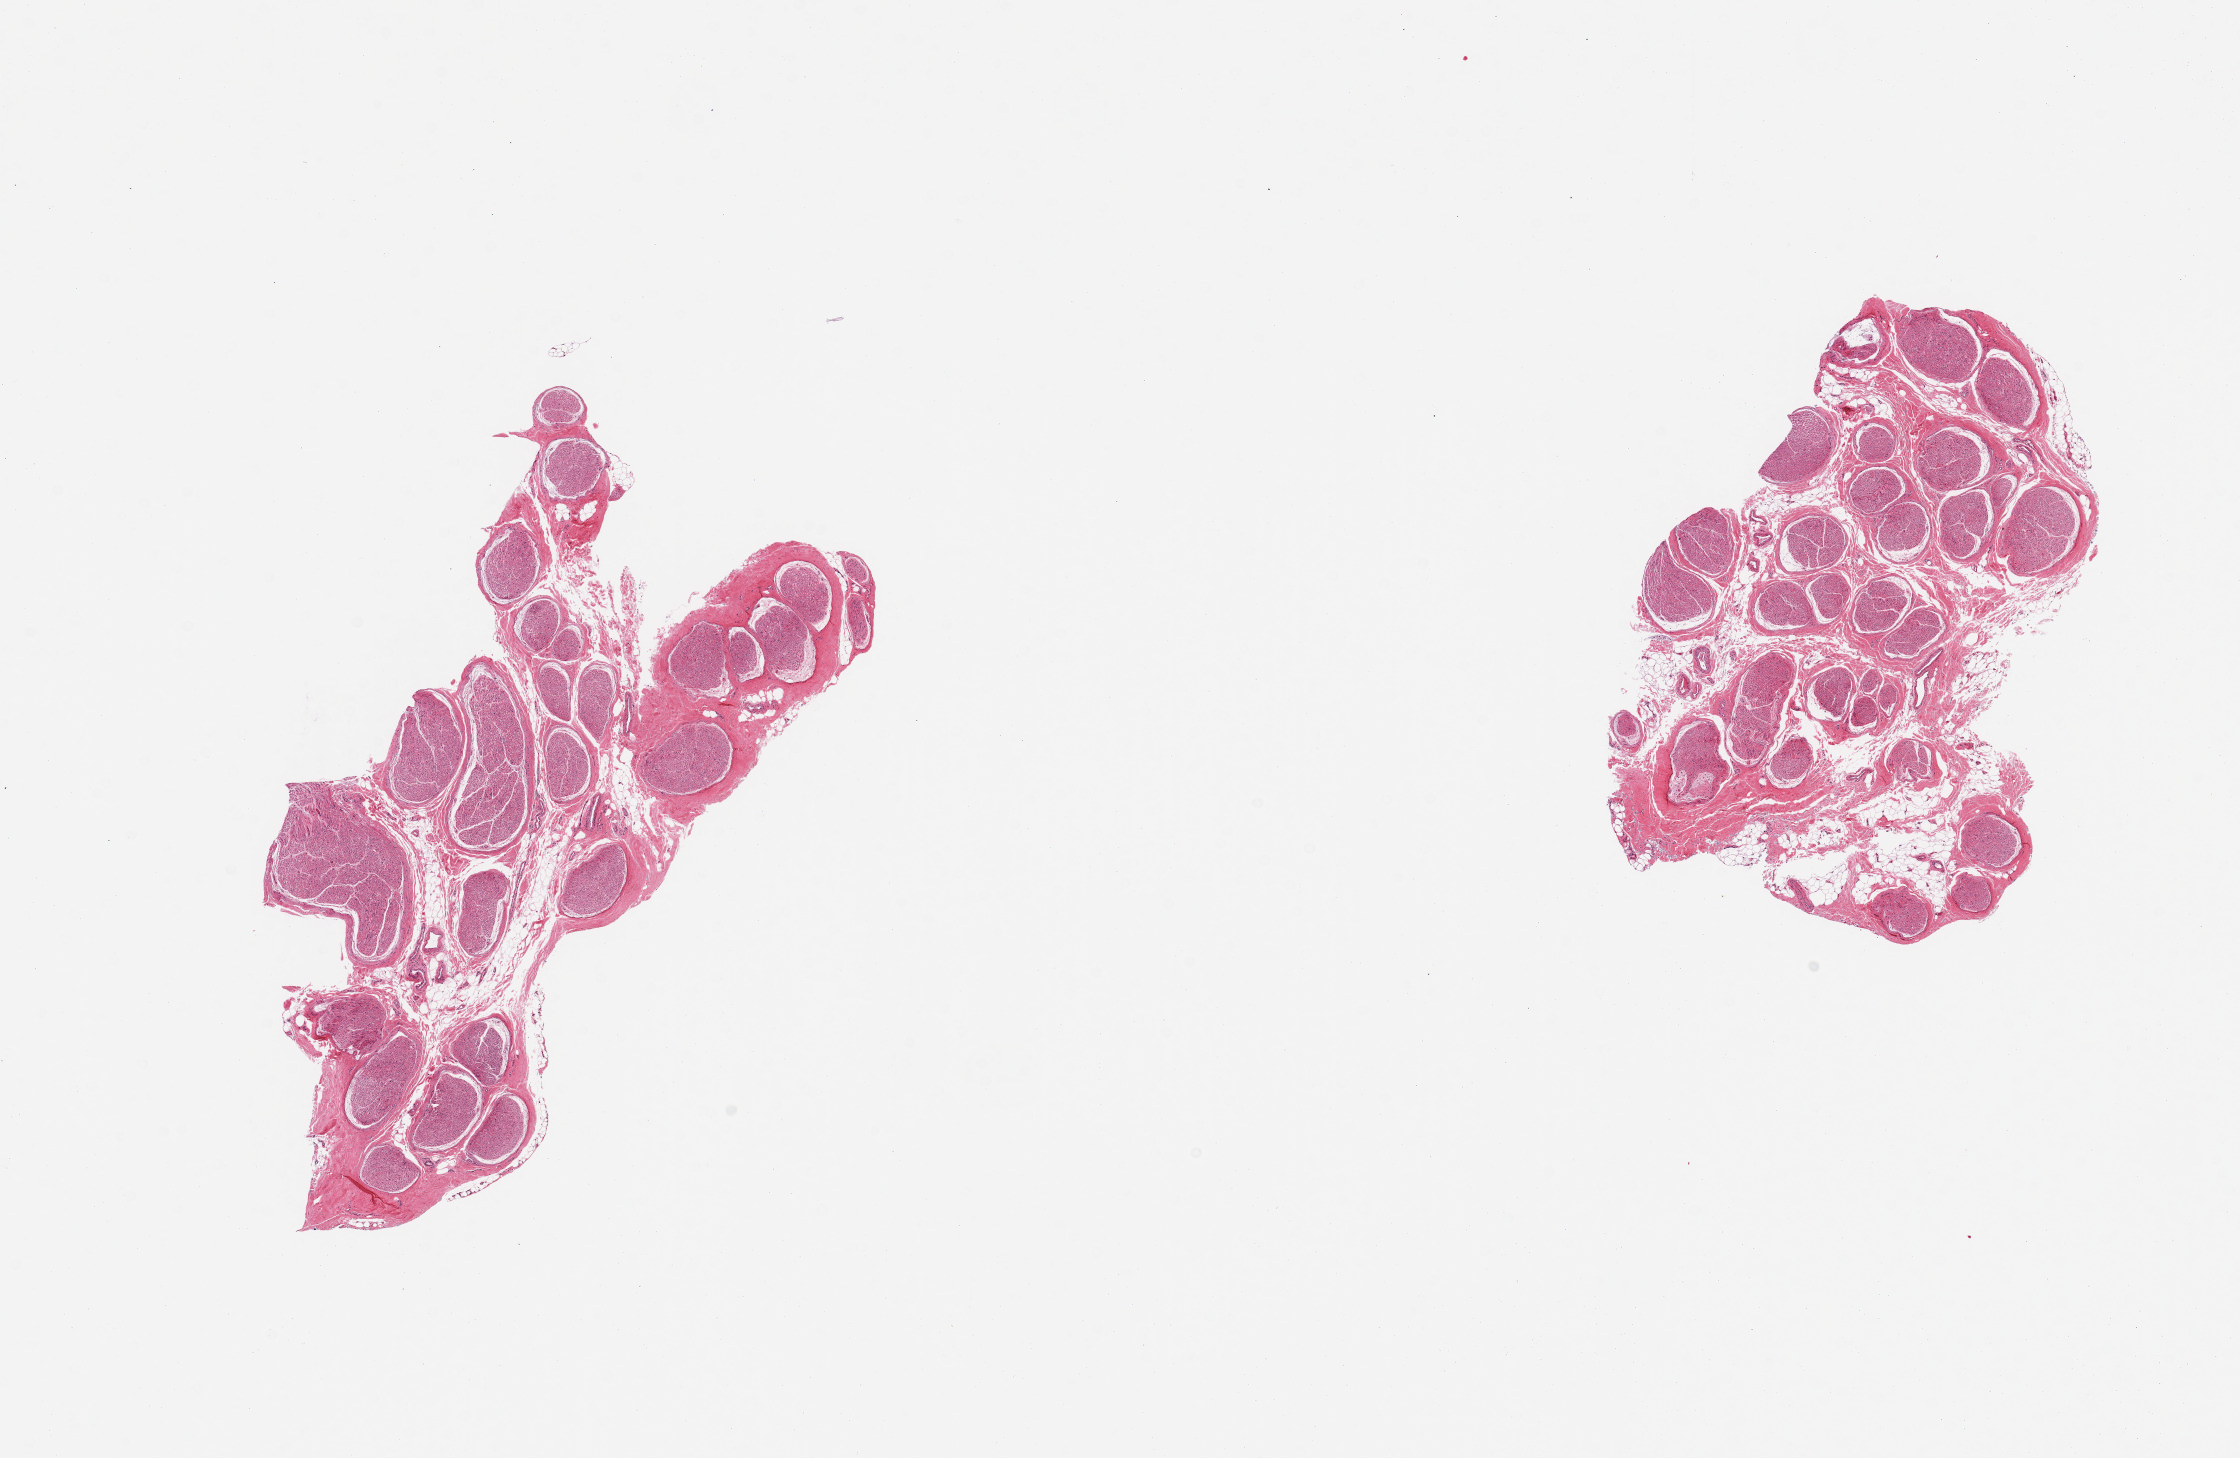
Whole-slide image, hematoxylin and eosin (H&E) stain, shown as a low-resolution overview of the whole scanned area (about 17.7 x 11.5 mm). PAXgene-fixed paraffin-embedded (PFPE) section. Sampled site (target tissue): tibial nerve. Donor tissue sample. Donor: male.
* pathologist's review note for this sample: 2 pieces; 10% & 20% internal fat content